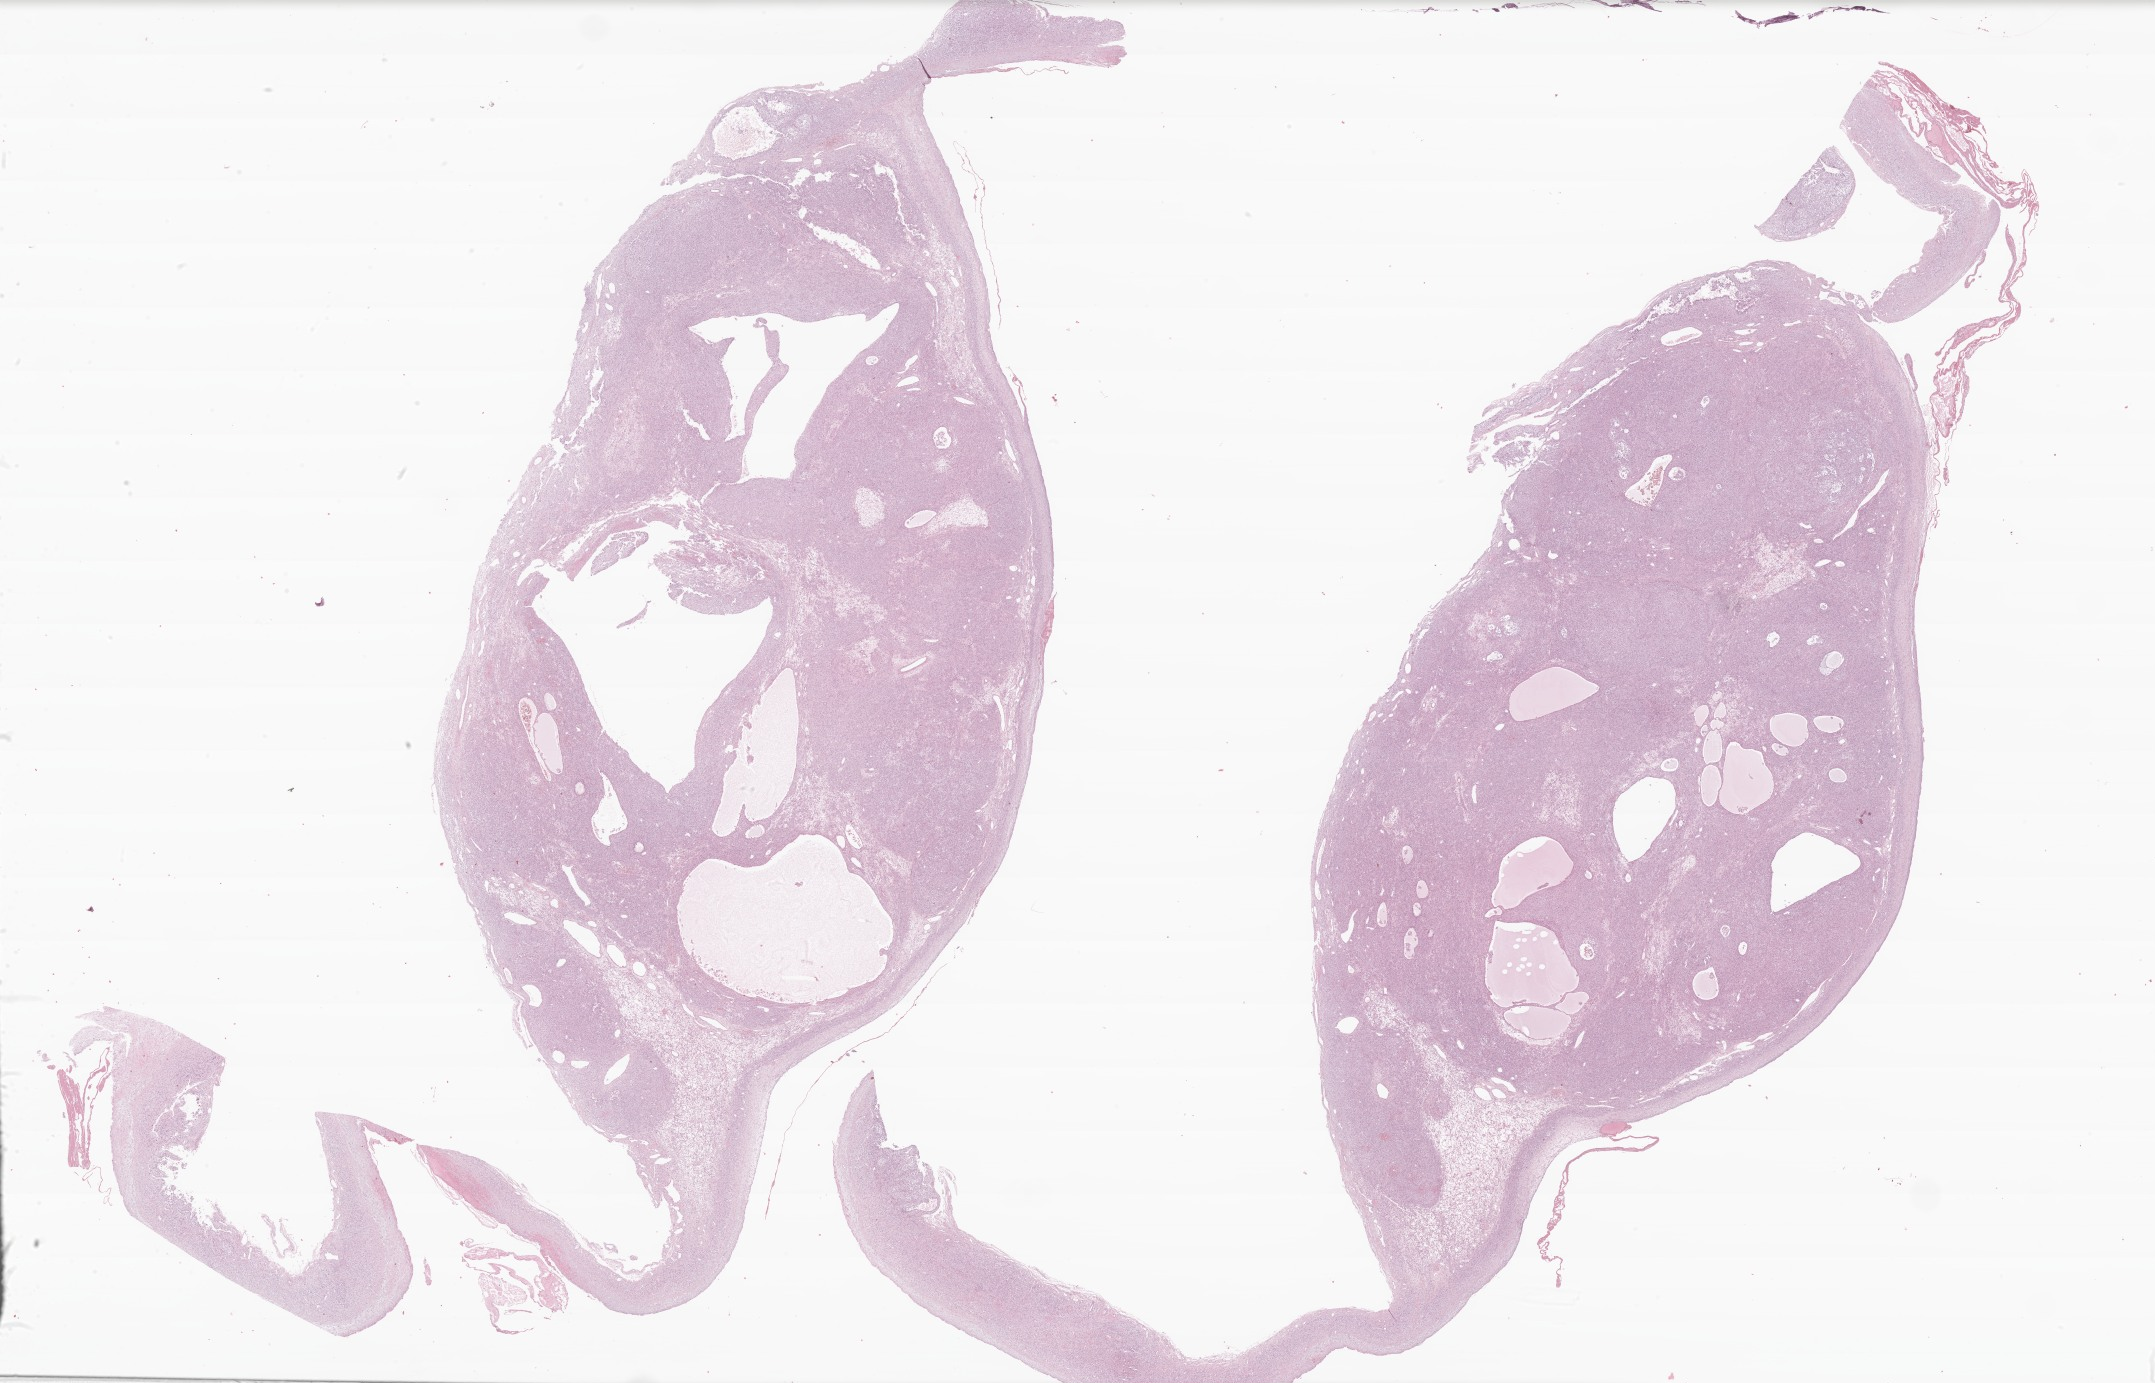
Hematoxylin and eosin (H&E) whole-slide image of tumor tissue from the ovary — shown as a low-resolution overview of the whole scanned area (about 36.3 x 23.3 mm); formalin-fixed, paraffin-embedded (FFPE) tissue. Patient female; age 107 months (8 years 11 months).
Diagnosis: Granulosa cell tumor, juvenile.